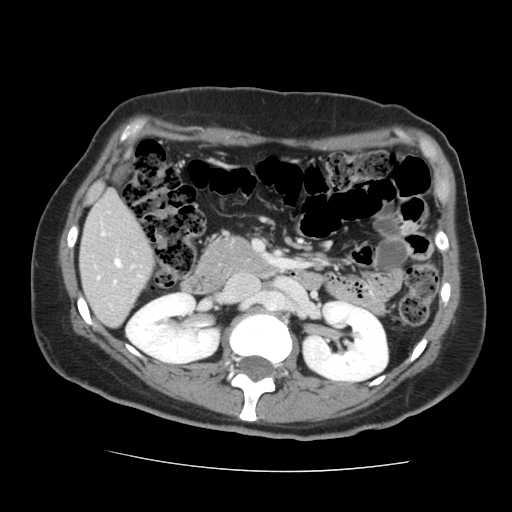
Contrast-enhanced abdominal CT, one axial slice. Slice 66 of 144 in the series (ordered by position). 120 kVp. Intravenous contrast given. Soft-tissue window (W 400 / L 40 HU). 512 × 512 image matrix. Female patient, age 46 years. From the clinical record (not read from this slice): diagnosis: colorectal cancer liver metastases, imaged before liver resection; multiple liver metastases: no.
Annotated regions visible in this slice (manually delineated by an expert):
- liver: bounding box [x1, y1, x2, y2] px = [80, 193, 153, 326]
- planned liver remnant (the part of the liver to remain after resection): [80, 193, 153, 325]
- portal vein (with intrahepatic branches): [97, 233, 120, 283]